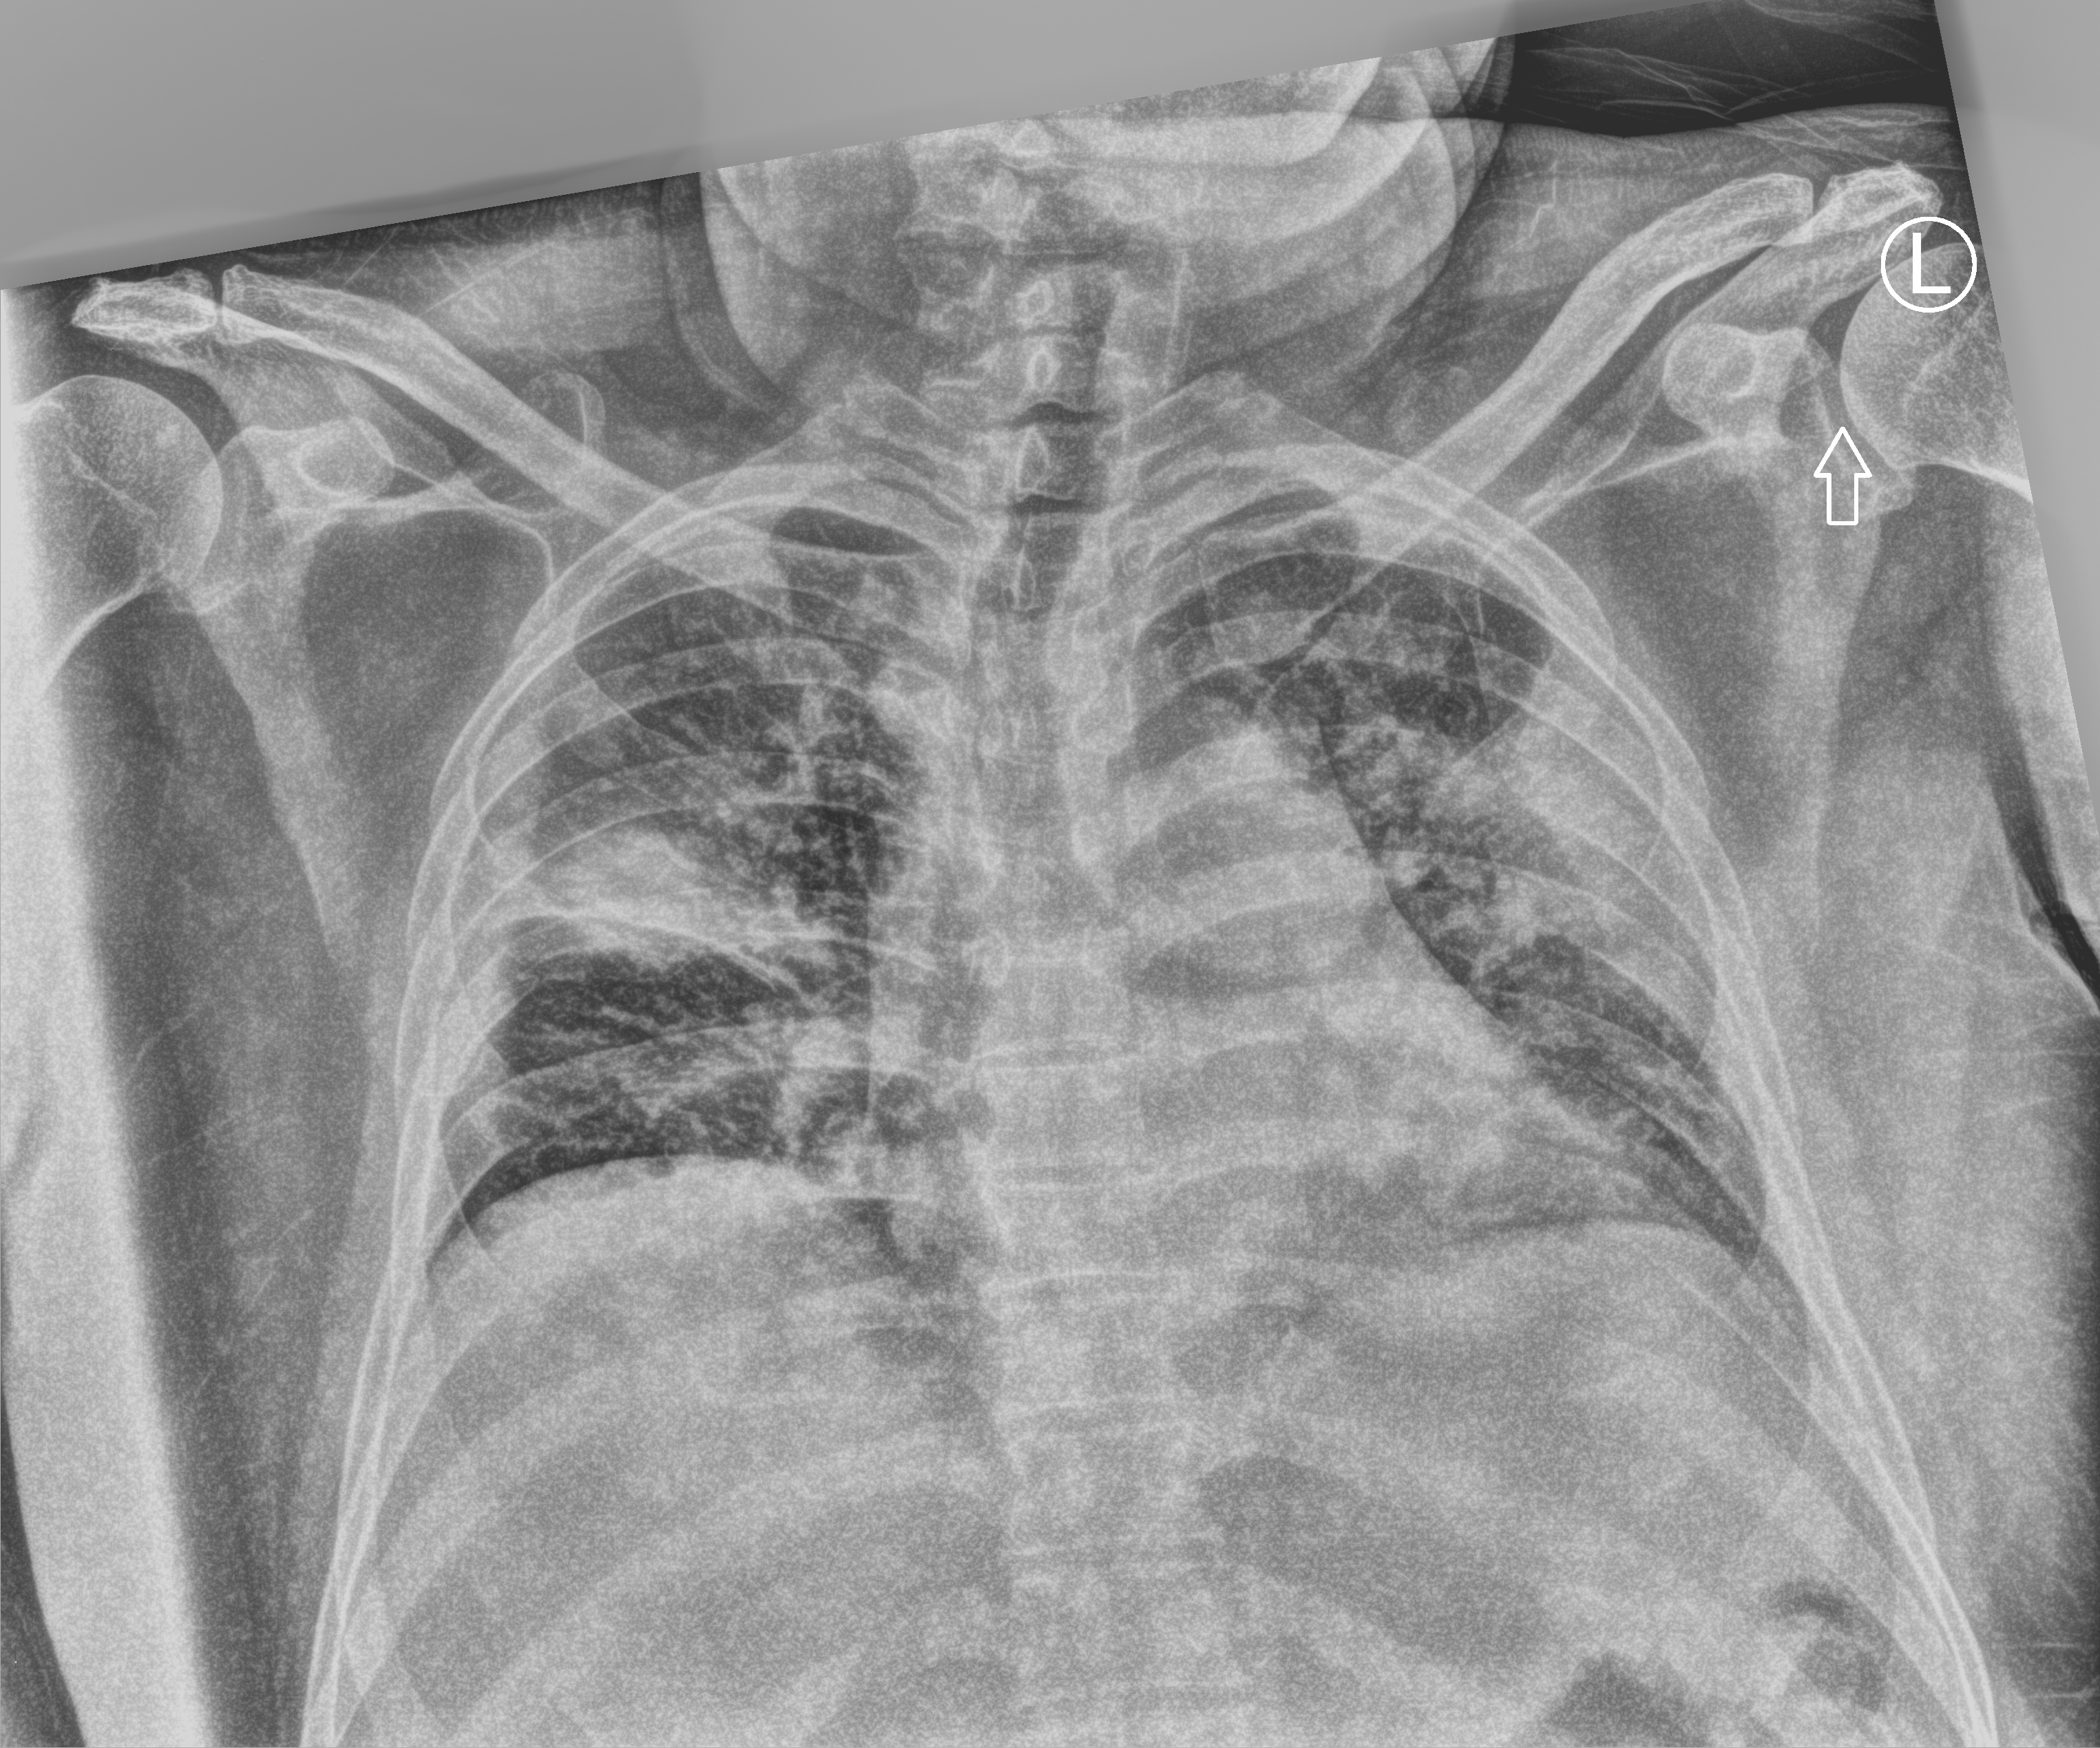
Chest X-ray (portable); anteroposterior (AP) projection. Patient hospitalised with COVID-19; male, aged 18–59 years.
Hospital-stay facts (about this admission, not read from this image; timing relative to this image not recorded): mechanically ventilated during this hospital stay: no; admitted to intensive care during this hospital stay: no.